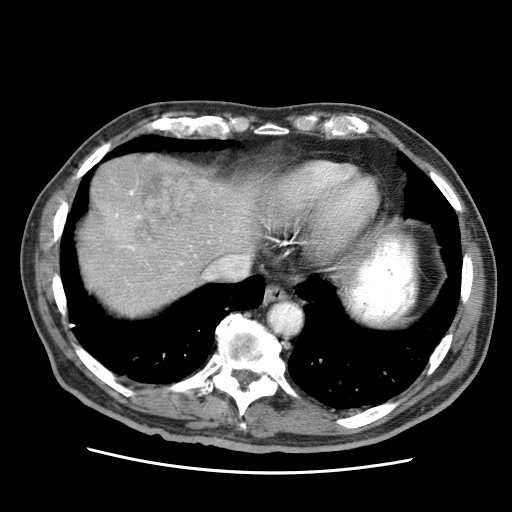
Contrast-enhanced abdominal CT (liver protocol), one axial slice; slice 58 of 75 in the series (ordered by position); reconstruction kernel STANDARD; 120 kVp; soft-tissue window (W 400 / L 40 HU); 2.5 mm slice thickness; 512 × 512 image matrix. Case-level facts recorded for this patient, not image findings: diagnosis: hepatocellular carcinoma (patient treated with transarterial chemoembolisation; whether this scan precedes or follows treatment is not stated here); TNM stage (as recorded): Stage-IIIA; Child-Pugh class: A; tumour differentiation: well differentiated; tumour nodularity: multinodular.
Structures marked on this image (semi-automatically segmented with operator editing):
- liver parenchyma outside the tumour (the mass and vessels are separate outlines, so this box may not span the whole liver): bounding box (x1, y1, x2, y2) in pixels: (80, 154, 260, 314)
- mass: (131, 173, 194, 249)
- liver vessels: (115, 190, 237, 265)